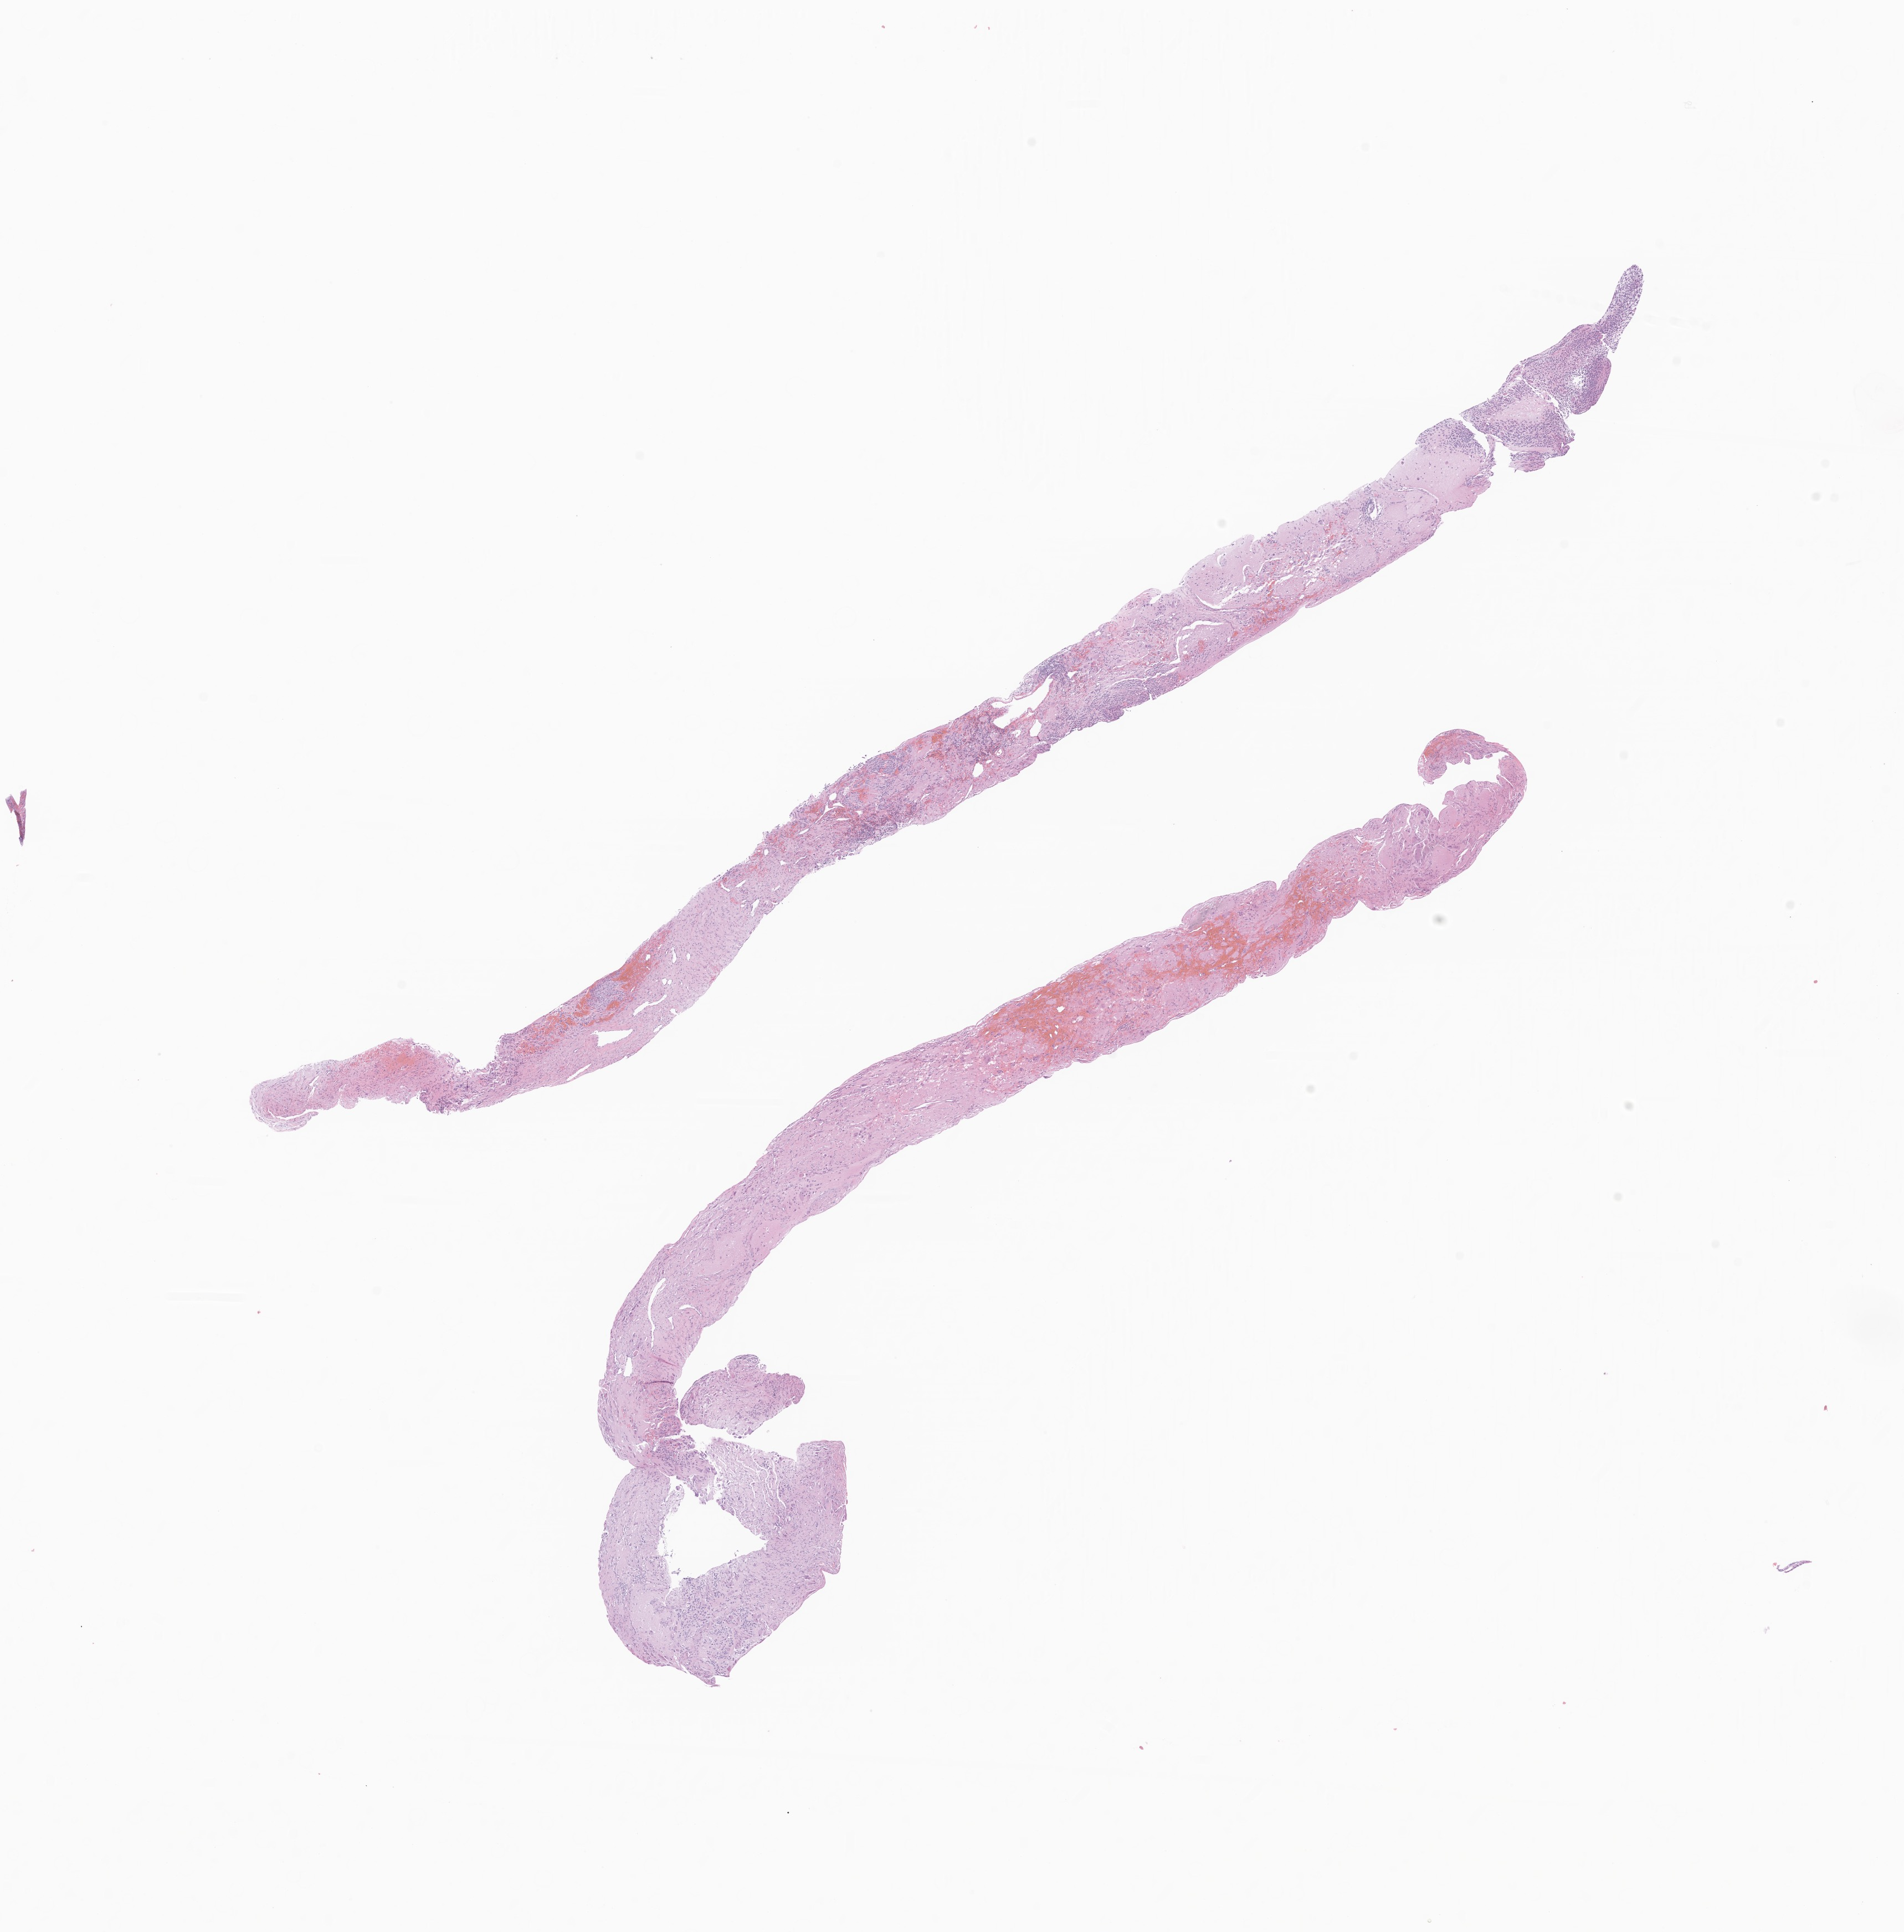
Digitized haematoxylin and eosin-stained section of tumor tissue from the posterior mediastinum — a low-resolution overview of the entire scanned area, about 14.5 x 14.7 mm; formalin-fixed, paraffin-embedded (FFPE) tissue. Female patient, age 51 months (4 years 3 months).
Diagnosis: Neuroblastoma, NOS.